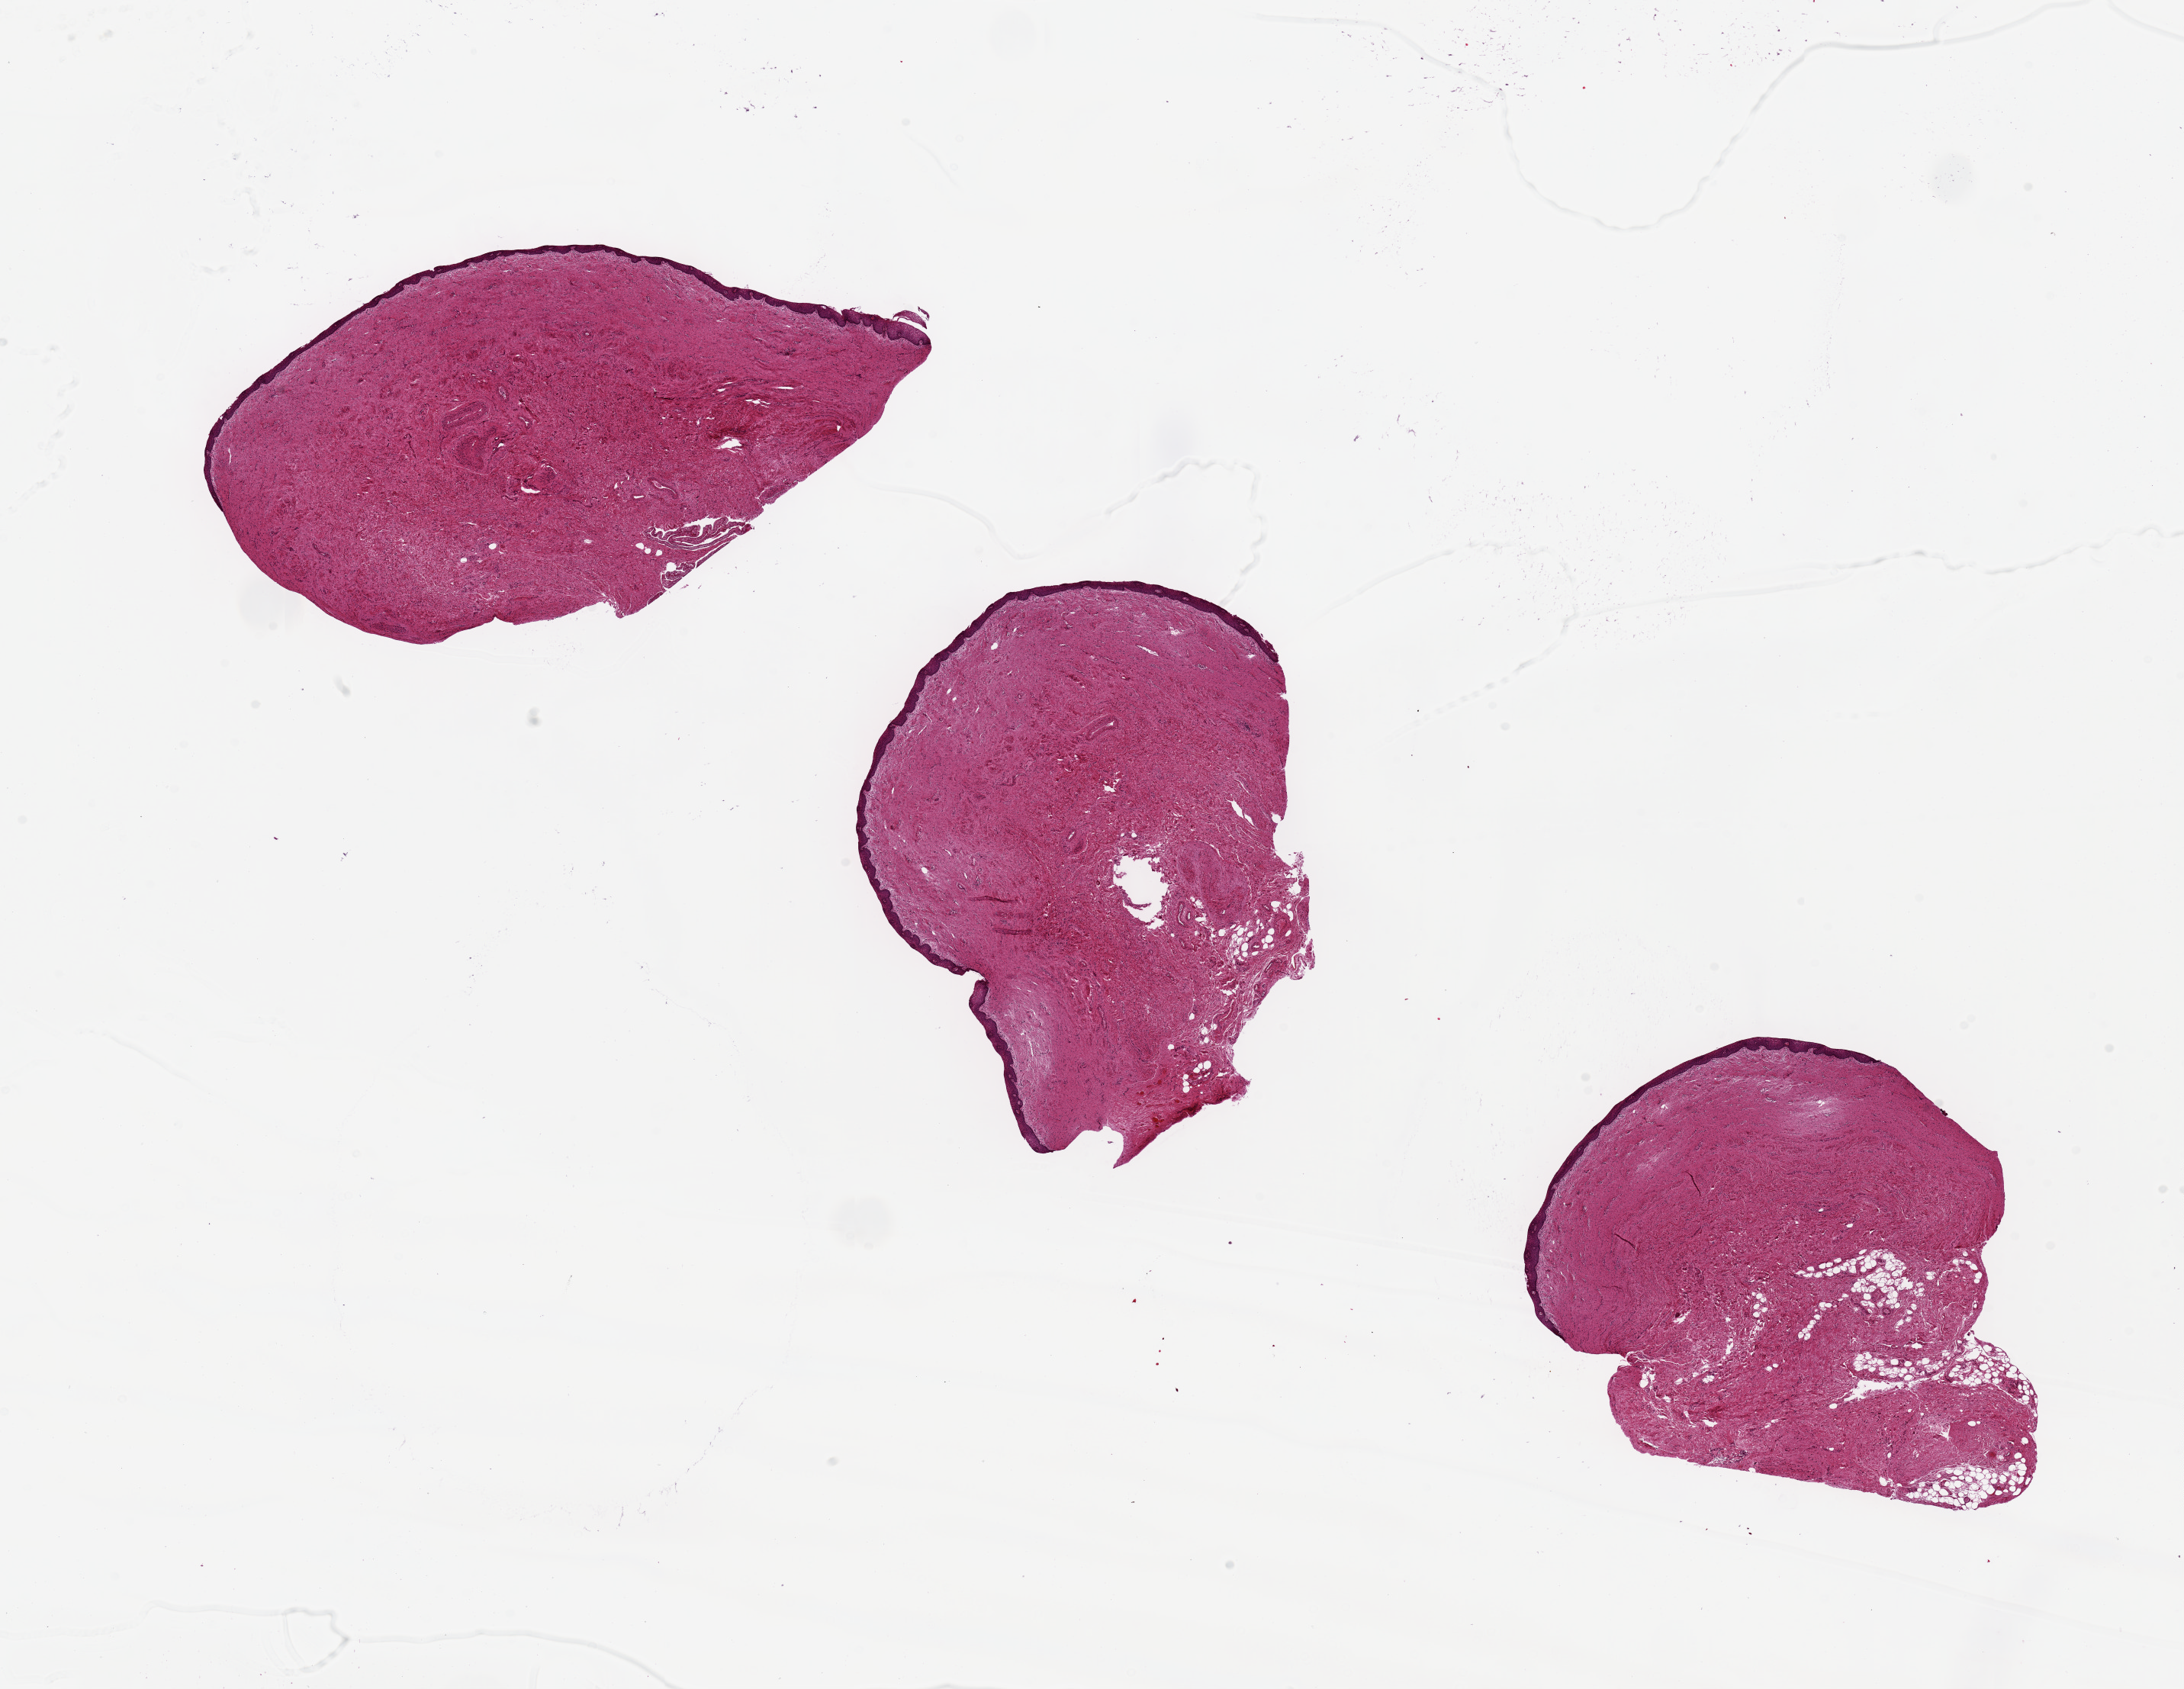
Whole-slide image, H&E stain — low-resolution overview of the scanned area, about 22.6 x 17.5 mm (from a 20x scan). PAXgene-fixed, paraffin-embedded tissue. Sampled site (target tissue): vagina. Tissue donor sample. Donor sex: female.
Reviewer comment on this tissue sample: Squamous mucosa ~2-3% of thickness.